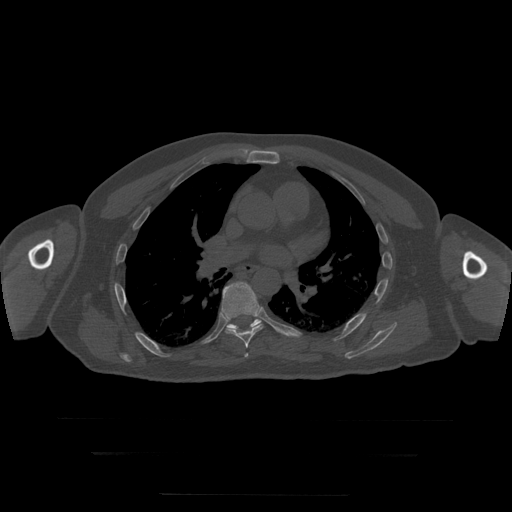
CT including the spine, one axial slice; position 181 of 397 along the scan axis; reconstruction kernel STANDARD; 120 kVp; bone window (W 1800 / L 400 HU); 1.25 mm slice thickness; 512 × 512 image matrix, field of view 510 × 510 mm. Patient age 73 years. Case-level facts recorded for this patient, not image findings: primary cancer: prostate.
Annotated regions visible in this slice (semi-automatic segmentation, software-assisted and operator-edited):
- T6 vertebra: bounding box [x1, y1, x2, y2] px = [245, 354, 249, 358]
- T7 vertebra: [222, 282, 263, 349]
- T8 vertebra: [227, 319, 284, 335]